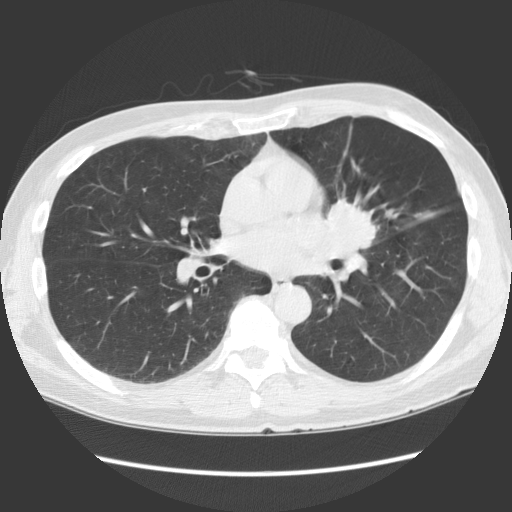
Low-dose screening chest CT, one axial slice. Position 67 of 136 along the scan axis. Reconstruction kernel STANDARD. 140 kVp. Lung window (W 1500 / L -600 HU). 512 × 512 image matrix.
Annotated regions visible in this slice (outlined manually by an expert reader):
- lesion 1 (tumor, hilum of left lung): bounding box <323,198,378,249> (left, top, right, bottom; pixels)